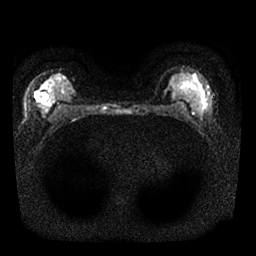
Breast MRI, one axial slice. Slice 15 of 25 in the series (ordered by position). Diffusion-weighted series; image 2 of 4 stored at this slice position (different b-values; order by instance number). 1.5 T. 4 mm slice thickness. 256 × 256 image matrix. Female patient.
Structures marked on this image (expert manual segmentation):
- tumour on diffusion-weighted imaging: bounding box [x1, y1, x2, y2] px = [38, 99, 41, 102]